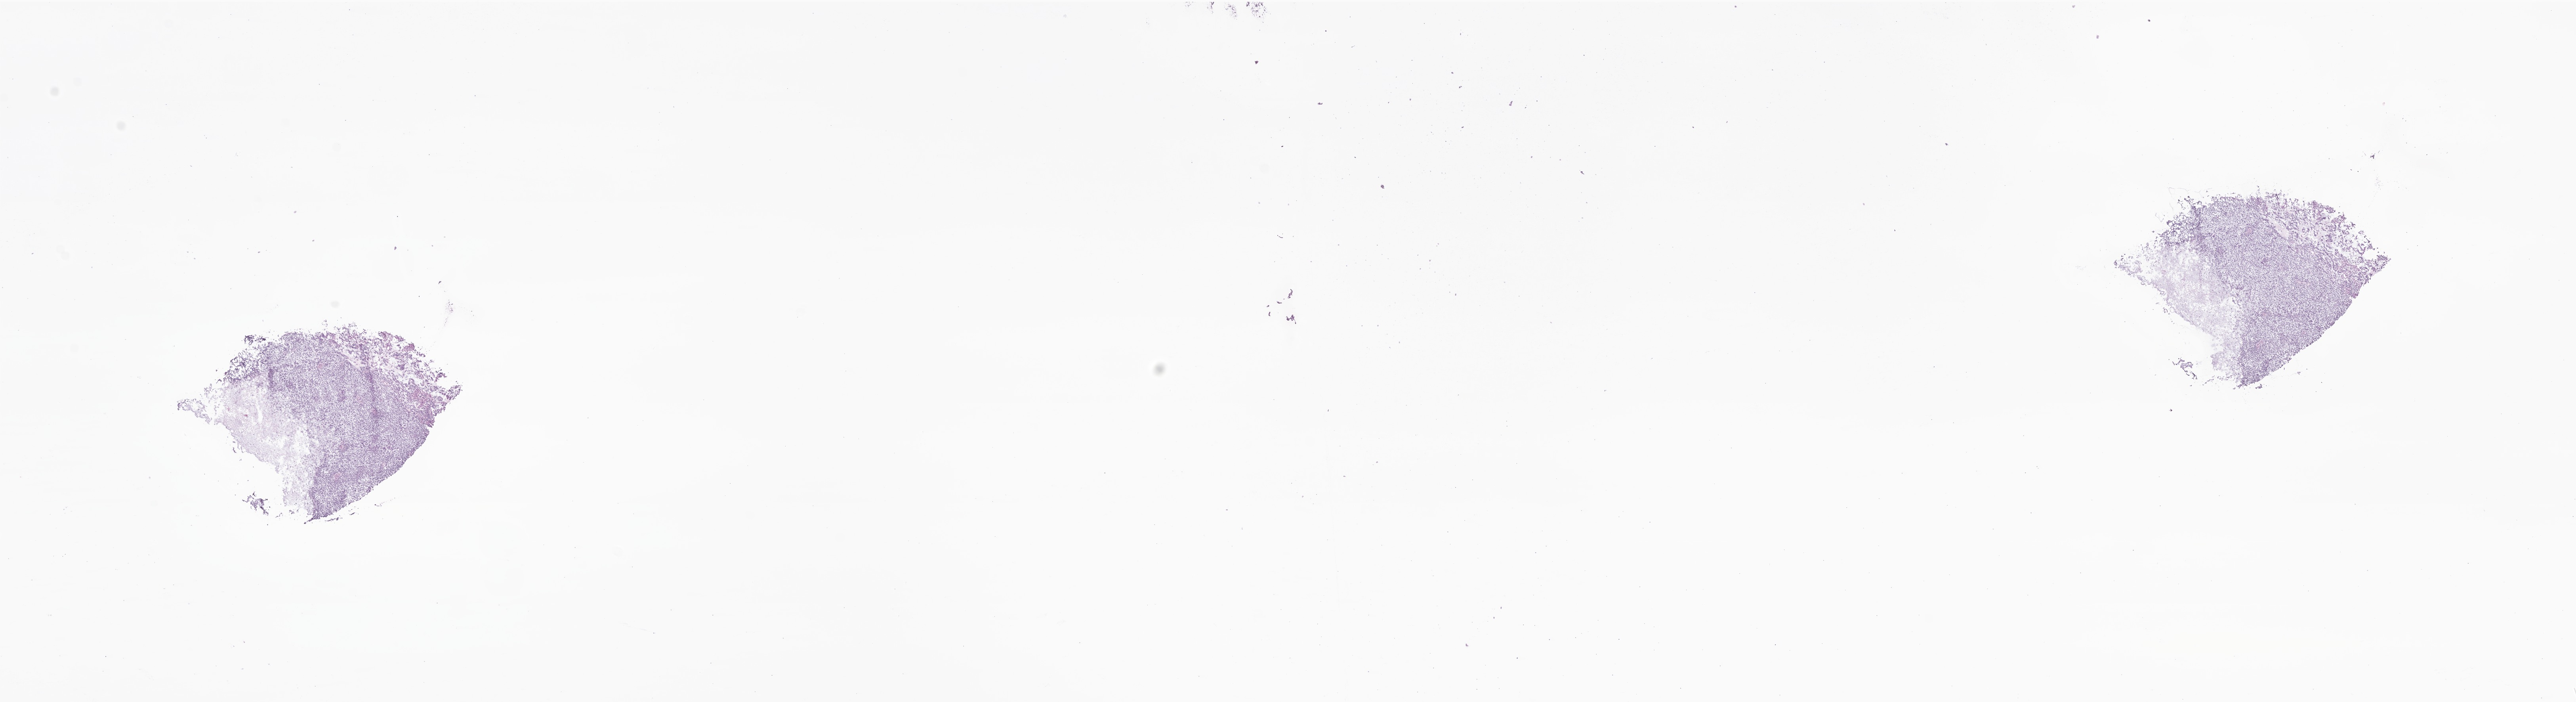
Hematoxylin and eosin (H&E) whole-slide image of tumor tissue from the parietal lobe, a low-resolution overview of the entire scanned area, about 27.4 x 7.5 mm. Frozen section (OCT-embedded). Patient female; age 412 days (about 1.1 years).
* diagnosis: Ependymoma, NOS